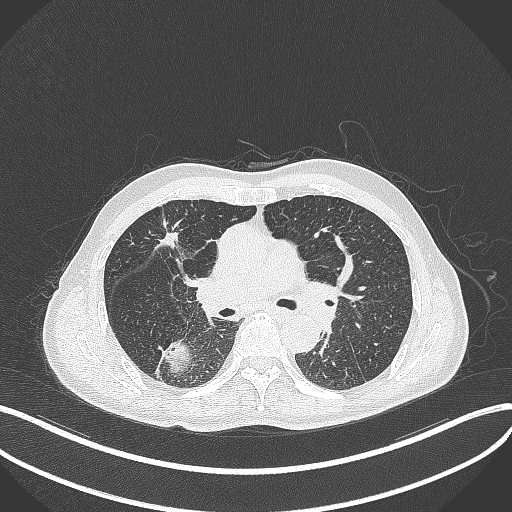
Chest CT, one axial slice. Slice 269 of 428 in the series (ordered by position). 120 kVp. Lung window (W 1500 / L -600 HU). 512 × 512 image matrix, field of view 400 × 400 mm. Male patient, age 79 years. Case-level facts recorded for this patient, not image findings: clinical TNM (as recorded): T3 N0 M0.
Structures marked on this image (rectangle marked by the reading radiologist):
- lung tumour (recorded histology: adenocarcinoma): bounding box (x1, y1, x2, y2) in pixels: (161, 339, 192, 376)